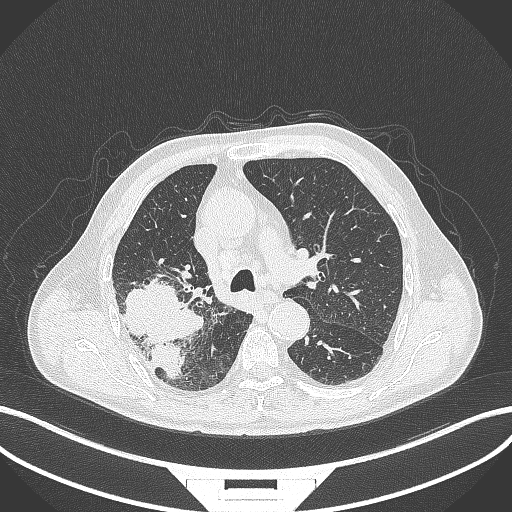
Chest CT, one axial slice; position 274 of 429 along the scan axis; reconstruction kernel B70f; 120 kVp; lung window (W 1500 / L -600 HU); 1 mm slice thickness; 512 × 512 image matrix, field of view 400 × 400 mm. Male patient, age 72 years. Case-level facts recorded for this patient, not image findings: clinical TNM (as recorded): T3 N2 M0.
Annotated regions visible in this slice (rectangle marked by the reading radiologist):
- lung tumour (recorded histology: adenocarcinoma): bounding box (x1, y1, x2, y2) in pixels: (123, 270, 206, 379)